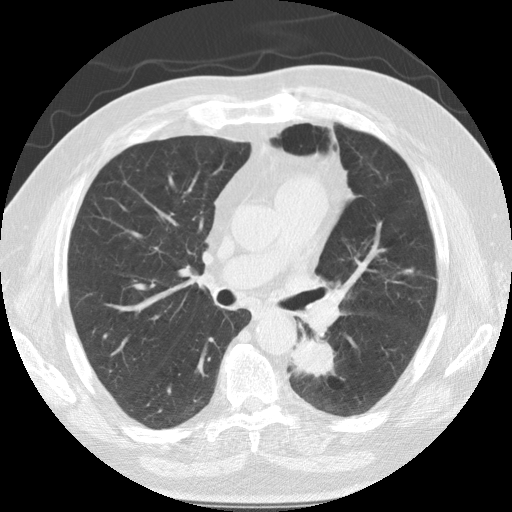
Low-dose screening chest CT, one axial slice; reconstruction kernel STANDARD; 120 kVp; lung window (W 1500 / L -600 HU); 2.5 mm slice thickness; 512 × 512 image matrix.
Outlined on this slice (expert manual segmentation):
- lesion 1 (tumor, lower lobe of left lung): bounding box <290,336,335,378> (left, top, right, bottom; pixels)